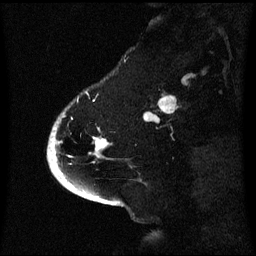
Breast MRI (dynamic contrast-enhanced), one sagittal slice. Position 15 of 60 along the scan axis. Dynamic contrast-enhanced series, image 2 of 3 at this slice position (ordered by acquisition). 1.5 T. TE 4.2 ms, TR 8.4 ms. 2.1 mm slice thickness. 256 × 256 image matrix. Female patient, age 53 years. From the clinical record (not read from this slice): setting: breast cancer imaged before/during neoadjuvant chemotherapy; receptor status: HR-positive, HER2-negative.
Annotated regions visible in this slice (semi-automatically segmented with operator editing):
- analysis volume of interest (the breast-tissue region the enhancement analysis was run in; not a lesion): bounding box <52,110,111,171> (left, top, right, bottom; pixels)
- tumour enhancement mask (voxels above the 70 % enhancement threshold inside the analysis volume of interest): <52,138,109,167>